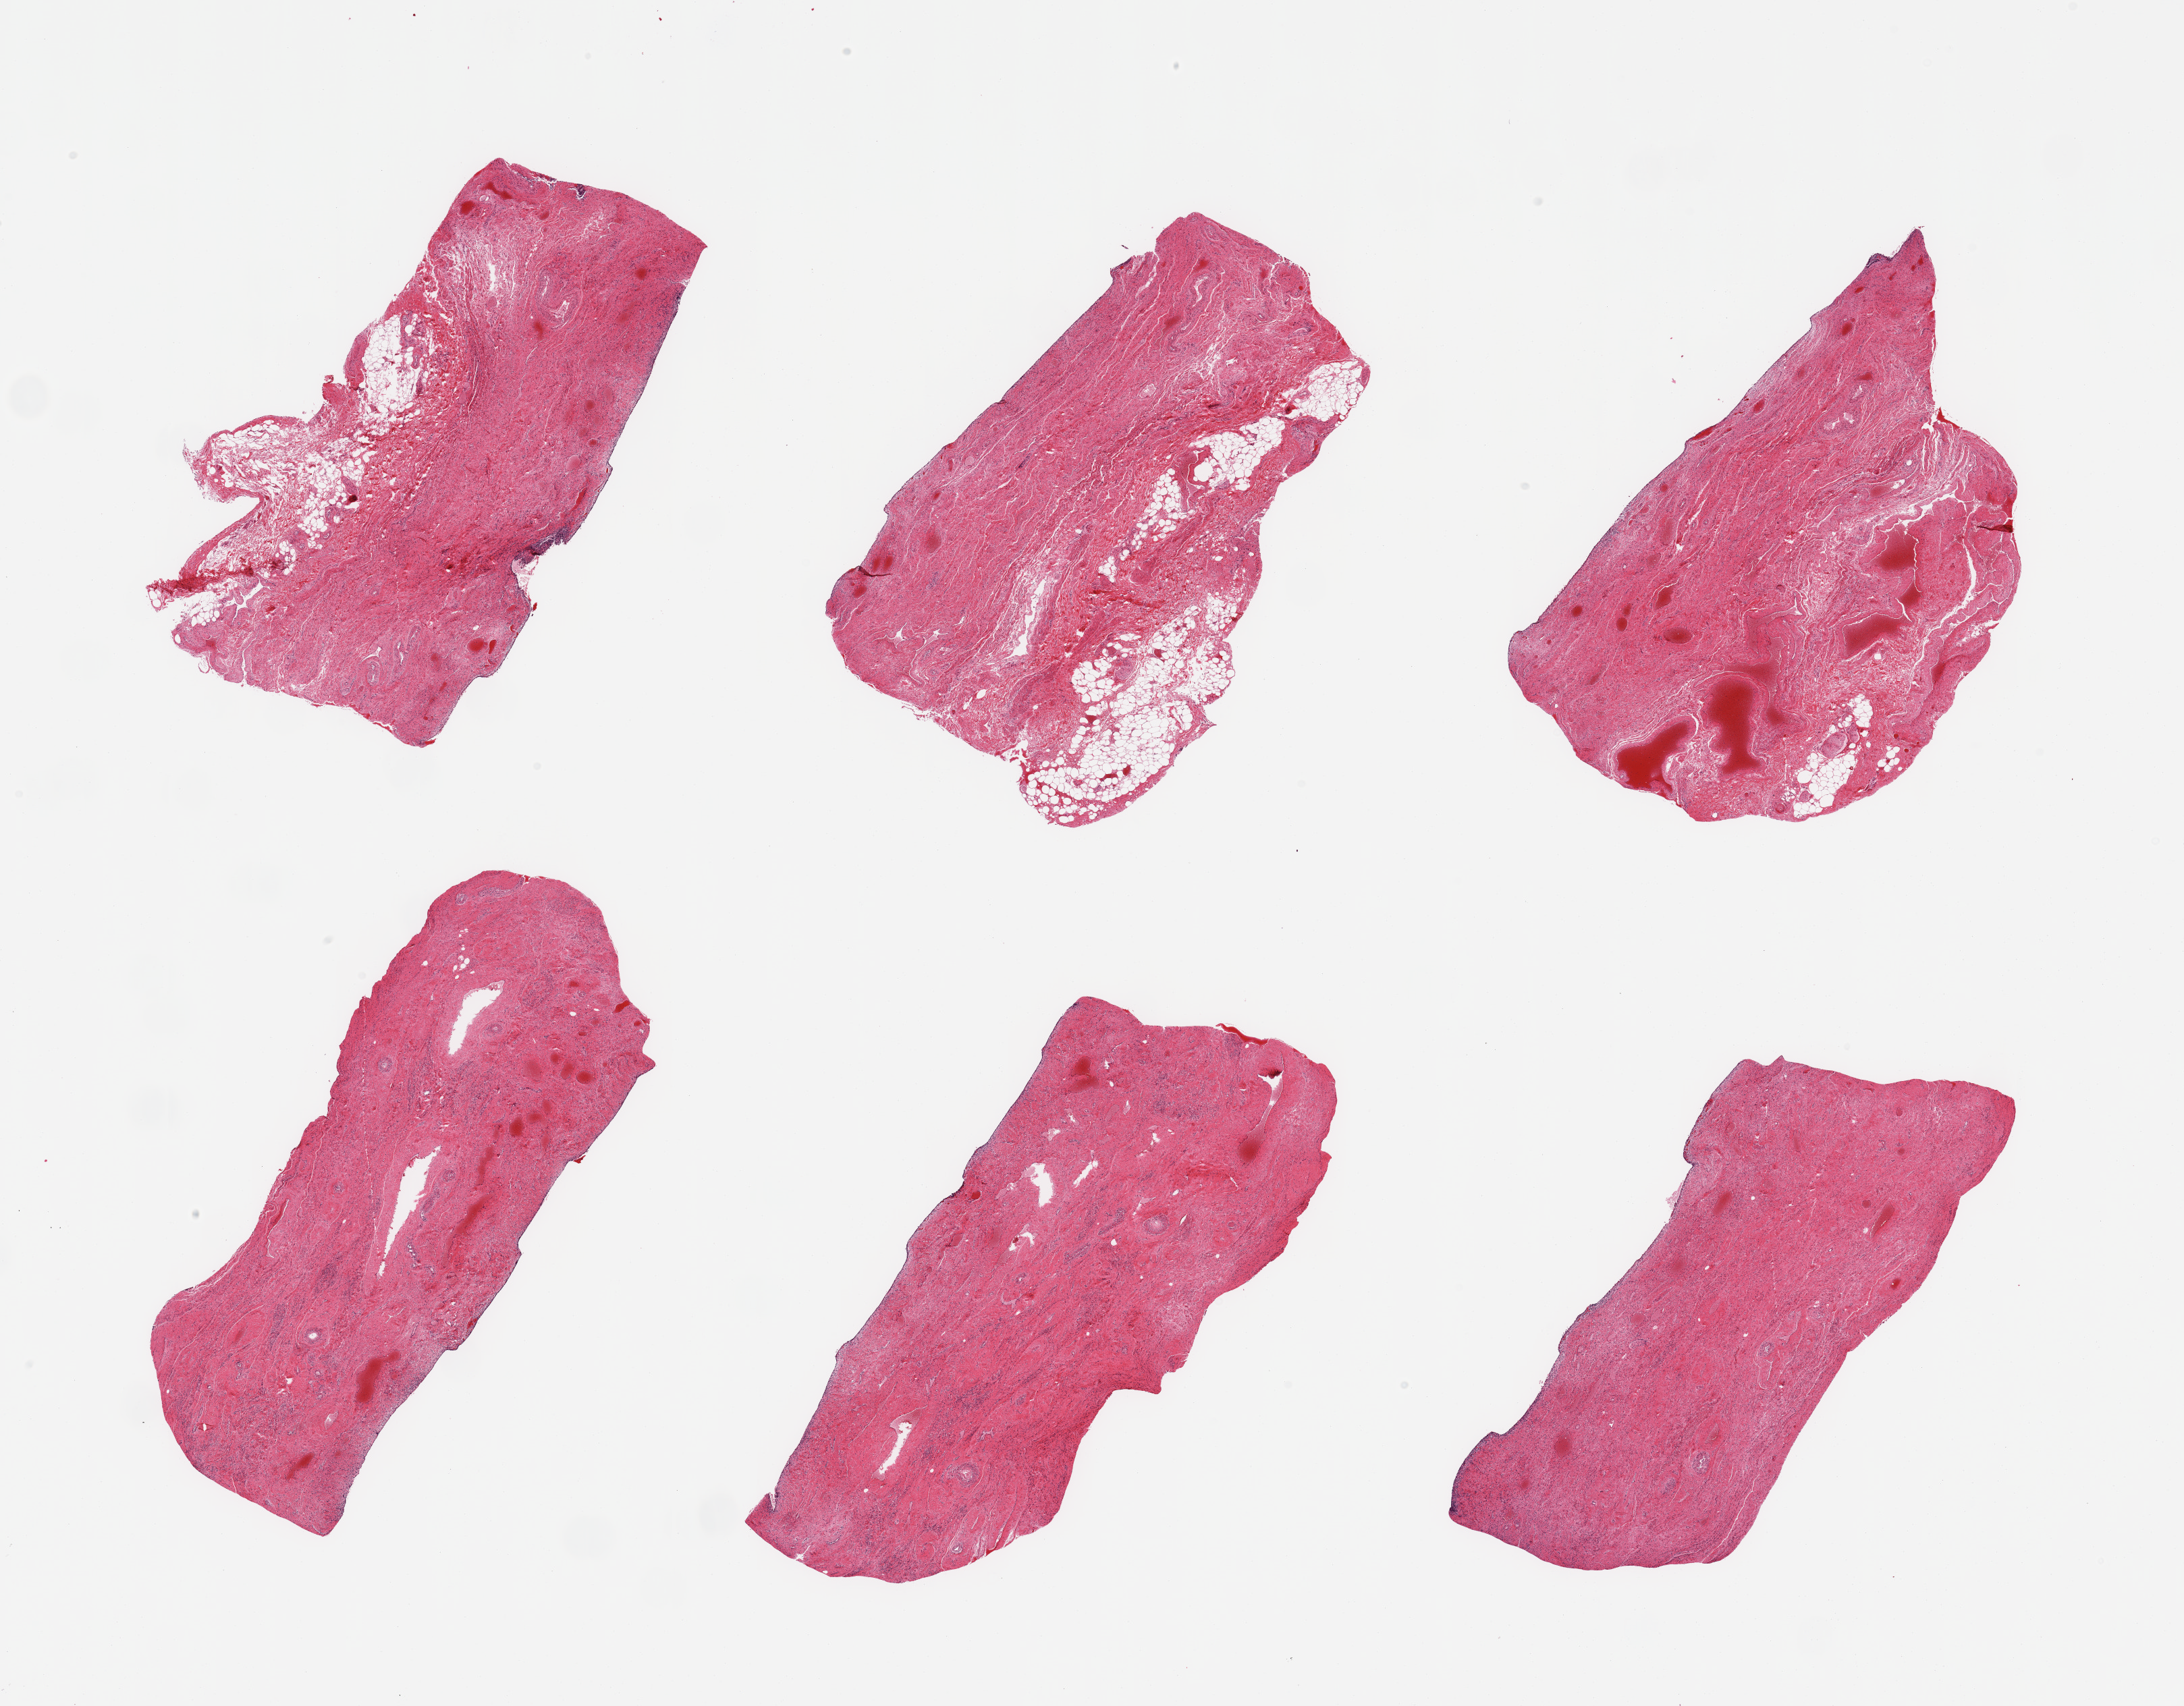
Whole-slide image, haematoxylin and eosin stain — a low-resolution overview of the entire scanned area, about 25.6 x 20.0 mm (from a 20x scan), PAXgene-fixed paraffin-embedded (PFPE) section, sampled site (target tissue): vagina, tissue donor sample. Female donor.
Reviewer comment on this tissue sample: 6 pieces; epithelium sloughed; deep aspect has up to 1.5mm thick fatty layer on 3 pieces.